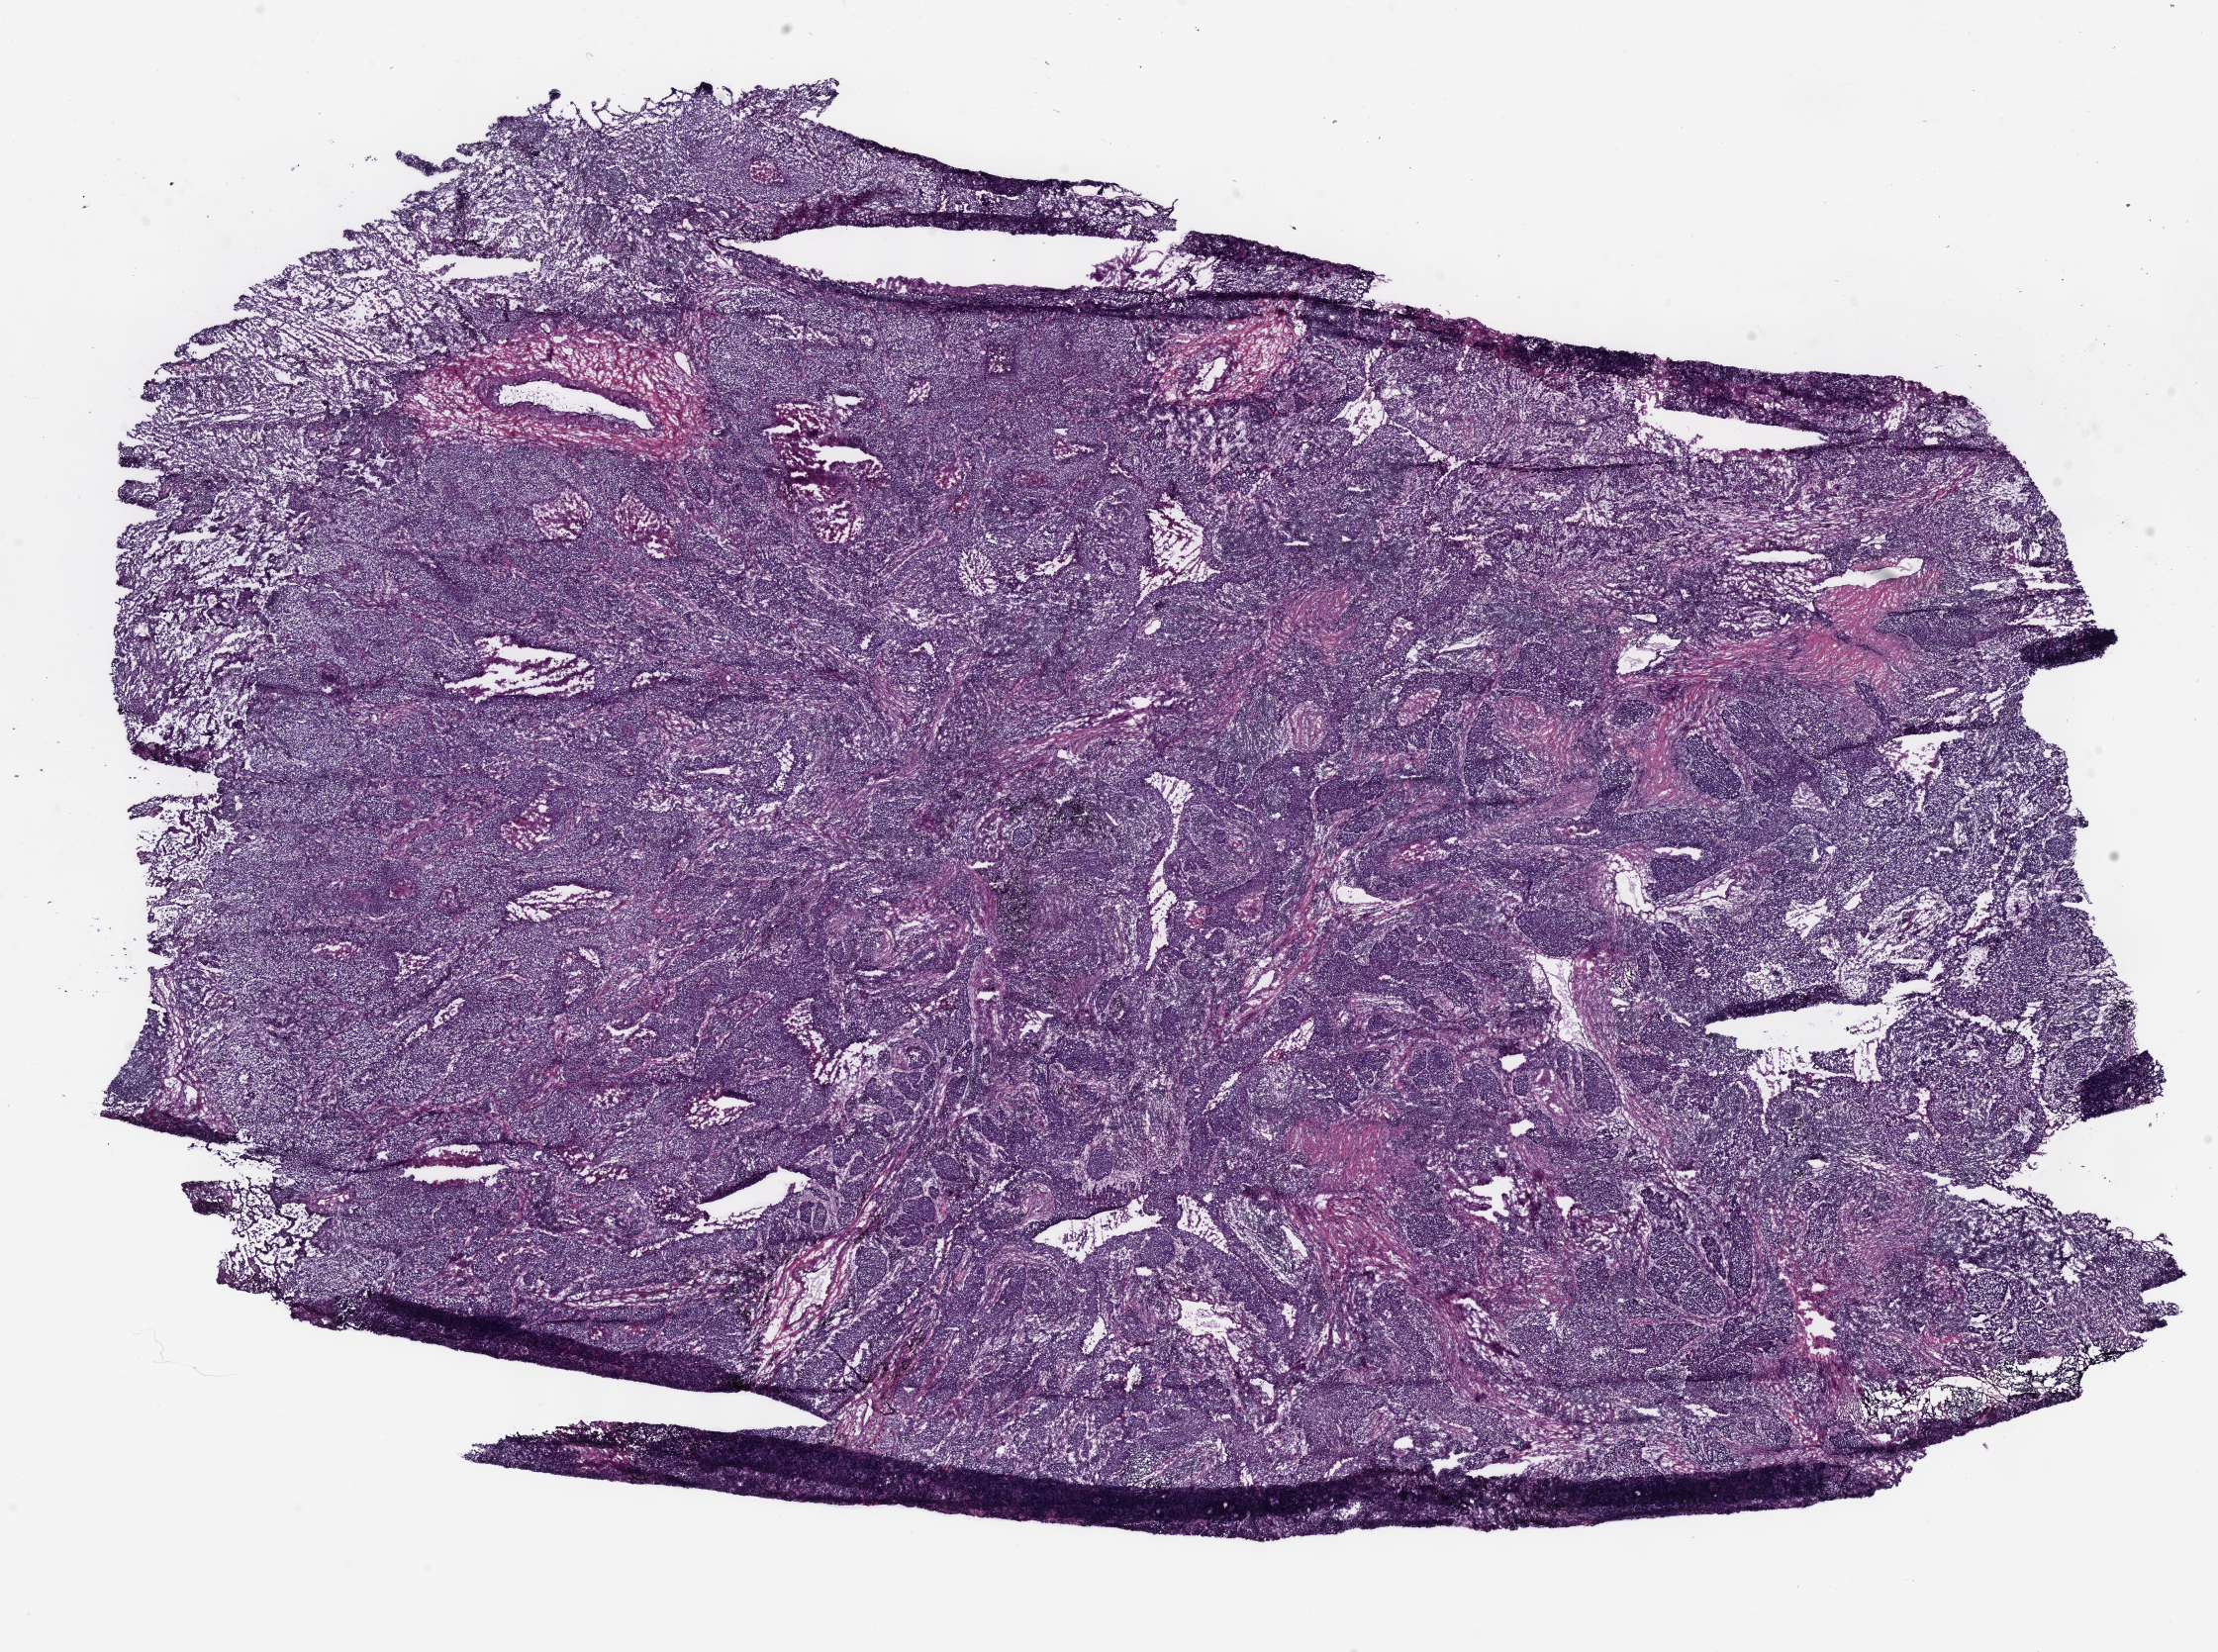
Hematoxylin and eosin (H&E) stained whole-slide image — a low-resolution overview of the entire scanned area, about 17.6 x 13.1 mm (from a 40x scan); frozen section; sample: primary tumour, lung. Male, age 72 years at initial diagnosis. Pathologist review of this section (percent, as recorded): tumour cells 75%, tumour nuclei 70%, normal cells 10%, stromal cells 10%, necrosis 5%.
Diagnosis: Squamous cell carcinoma, NOS (upper lobe, lung). AJCC pathologic stage: IA (7th edition).